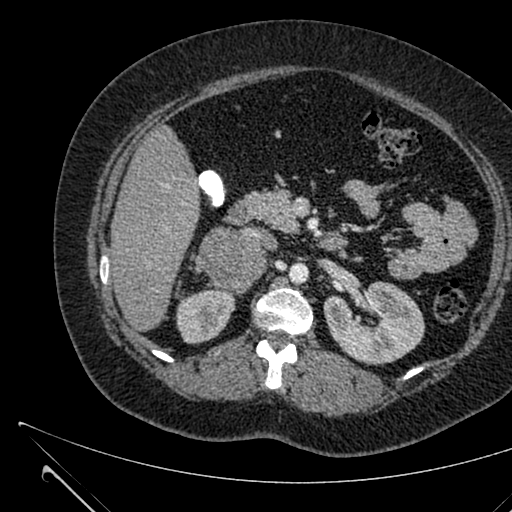
Contrast-enhanced abdominal CT, one axial slice; slice 369 of 731 in the series (ordered by position); 120 kVp; soft-tissue window (W 400 / L 40 HU); 1 mm slice thickness; 512 × 512 image matrix, field of view 376 × 376 mm. Female patient, age 36 years. From the clinical record (not read from this slice): diagnosis: adrenocortical carcinoma; tumour side: right adrenal; tumour size at pathology: 10 cm; Ki-67 index: 20 %; stage (as recorded): 4.
Outlined on this slice (semi-automatic segmentation, software-assisted and operator-edited):
- mass: bounding box [x1, y1, x2, y2] px = [198, 228, 266, 292]